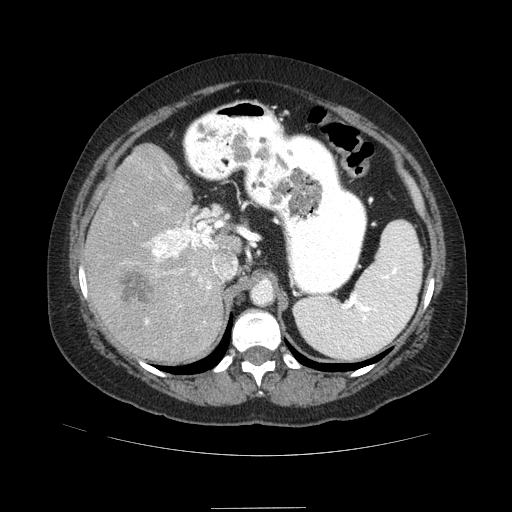
Contrast-enhanced abdominal CT (liver protocol), one axial slice. Slice 55 of 89 in the series (ordered by position). Reconstruction kernel STANDARD. 120 kVp. Soft-tissue window (W 400 / L 40 HU). 512 × 512 image matrix, field of view 400 × 400 mm. Case-level facts recorded for this patient, not image findings: diagnosis: hepatocellular carcinoma (patient treated with transarterial chemoembolisation; whether this scan precedes or follows treatment is not stated here); TNM stage (as recorded): Stage-IIIB; Child-Pugh class: A; tumour nodularity: multinodular.
Annotated regions visible in this slice (semi-automatic segmentation, software-assisted and operator-edited):
- liver parenchyma outside the tumour (the mass and vessels are separate outlines, so this box may not span the whole liver): bounding box [x1, y1, x2, y2] px = [82, 144, 240, 362]
- mass: [119, 268, 156, 311]
- liver vessels: [134, 168, 227, 324]